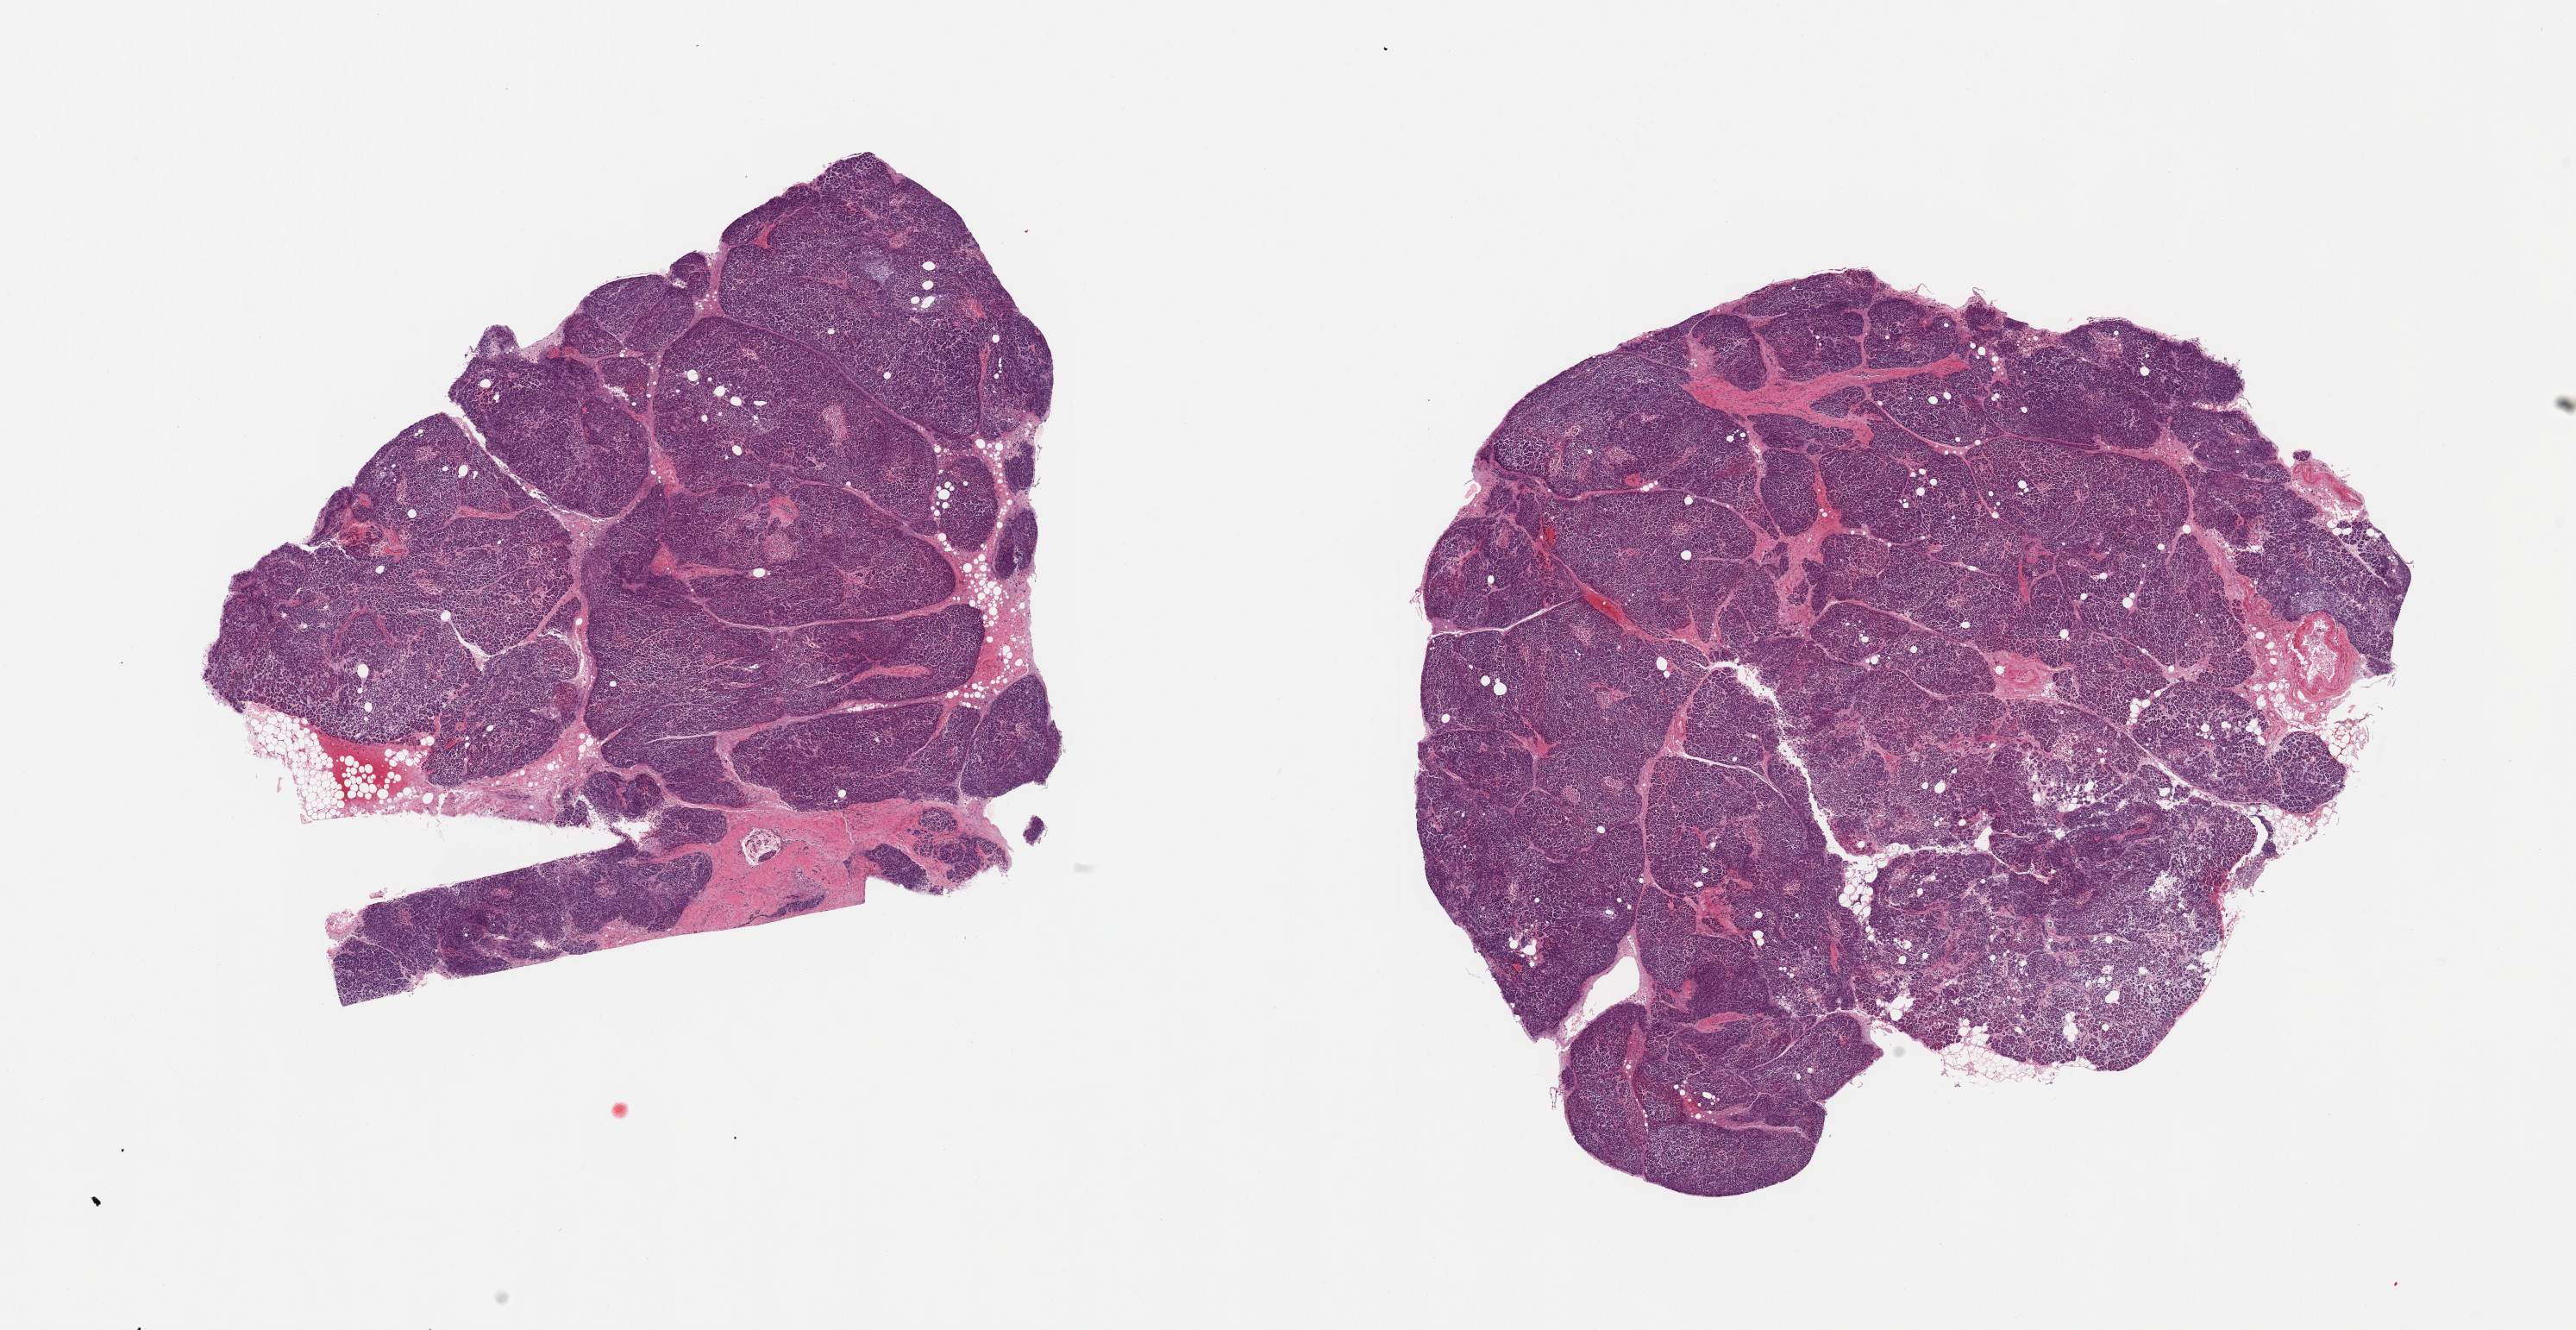
Hematoxylin and eosin (H&E) whole-slide image — low-resolution overview of the scanned area, about 23.6 x 12.2 mm (acquisition: 20x scan), PAXgene-fixed paraffin-embedded (PFPE) section, target tissue: pancreas, donor tissue sample.
Review note (as recorded): 2 pieces, moderate saponification, Islets badly degraded.